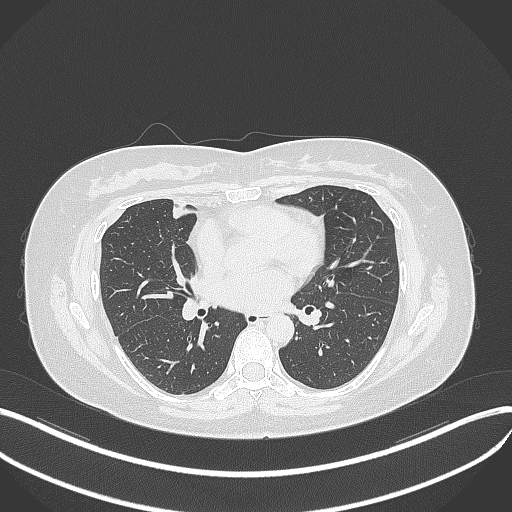
Chest CT, one axial slice; slice 153 of 273 in the series (ordered by position); reconstruction kernel B70f; 120 kVp; lung window (W 1500 / L -600 HU); 512 × 512 image matrix. Patient: female, 42 years. From the clinical record (not read from this slice): clinical TNM (as recorded): T1b N0 M0.
Annotated regions visible in this slice (rectangle marked by the reading radiologist):
- lung tumour (recorded histology: adenocarcinoma): bounding box <169,200,195,225> (left, top, right, bottom; pixels)